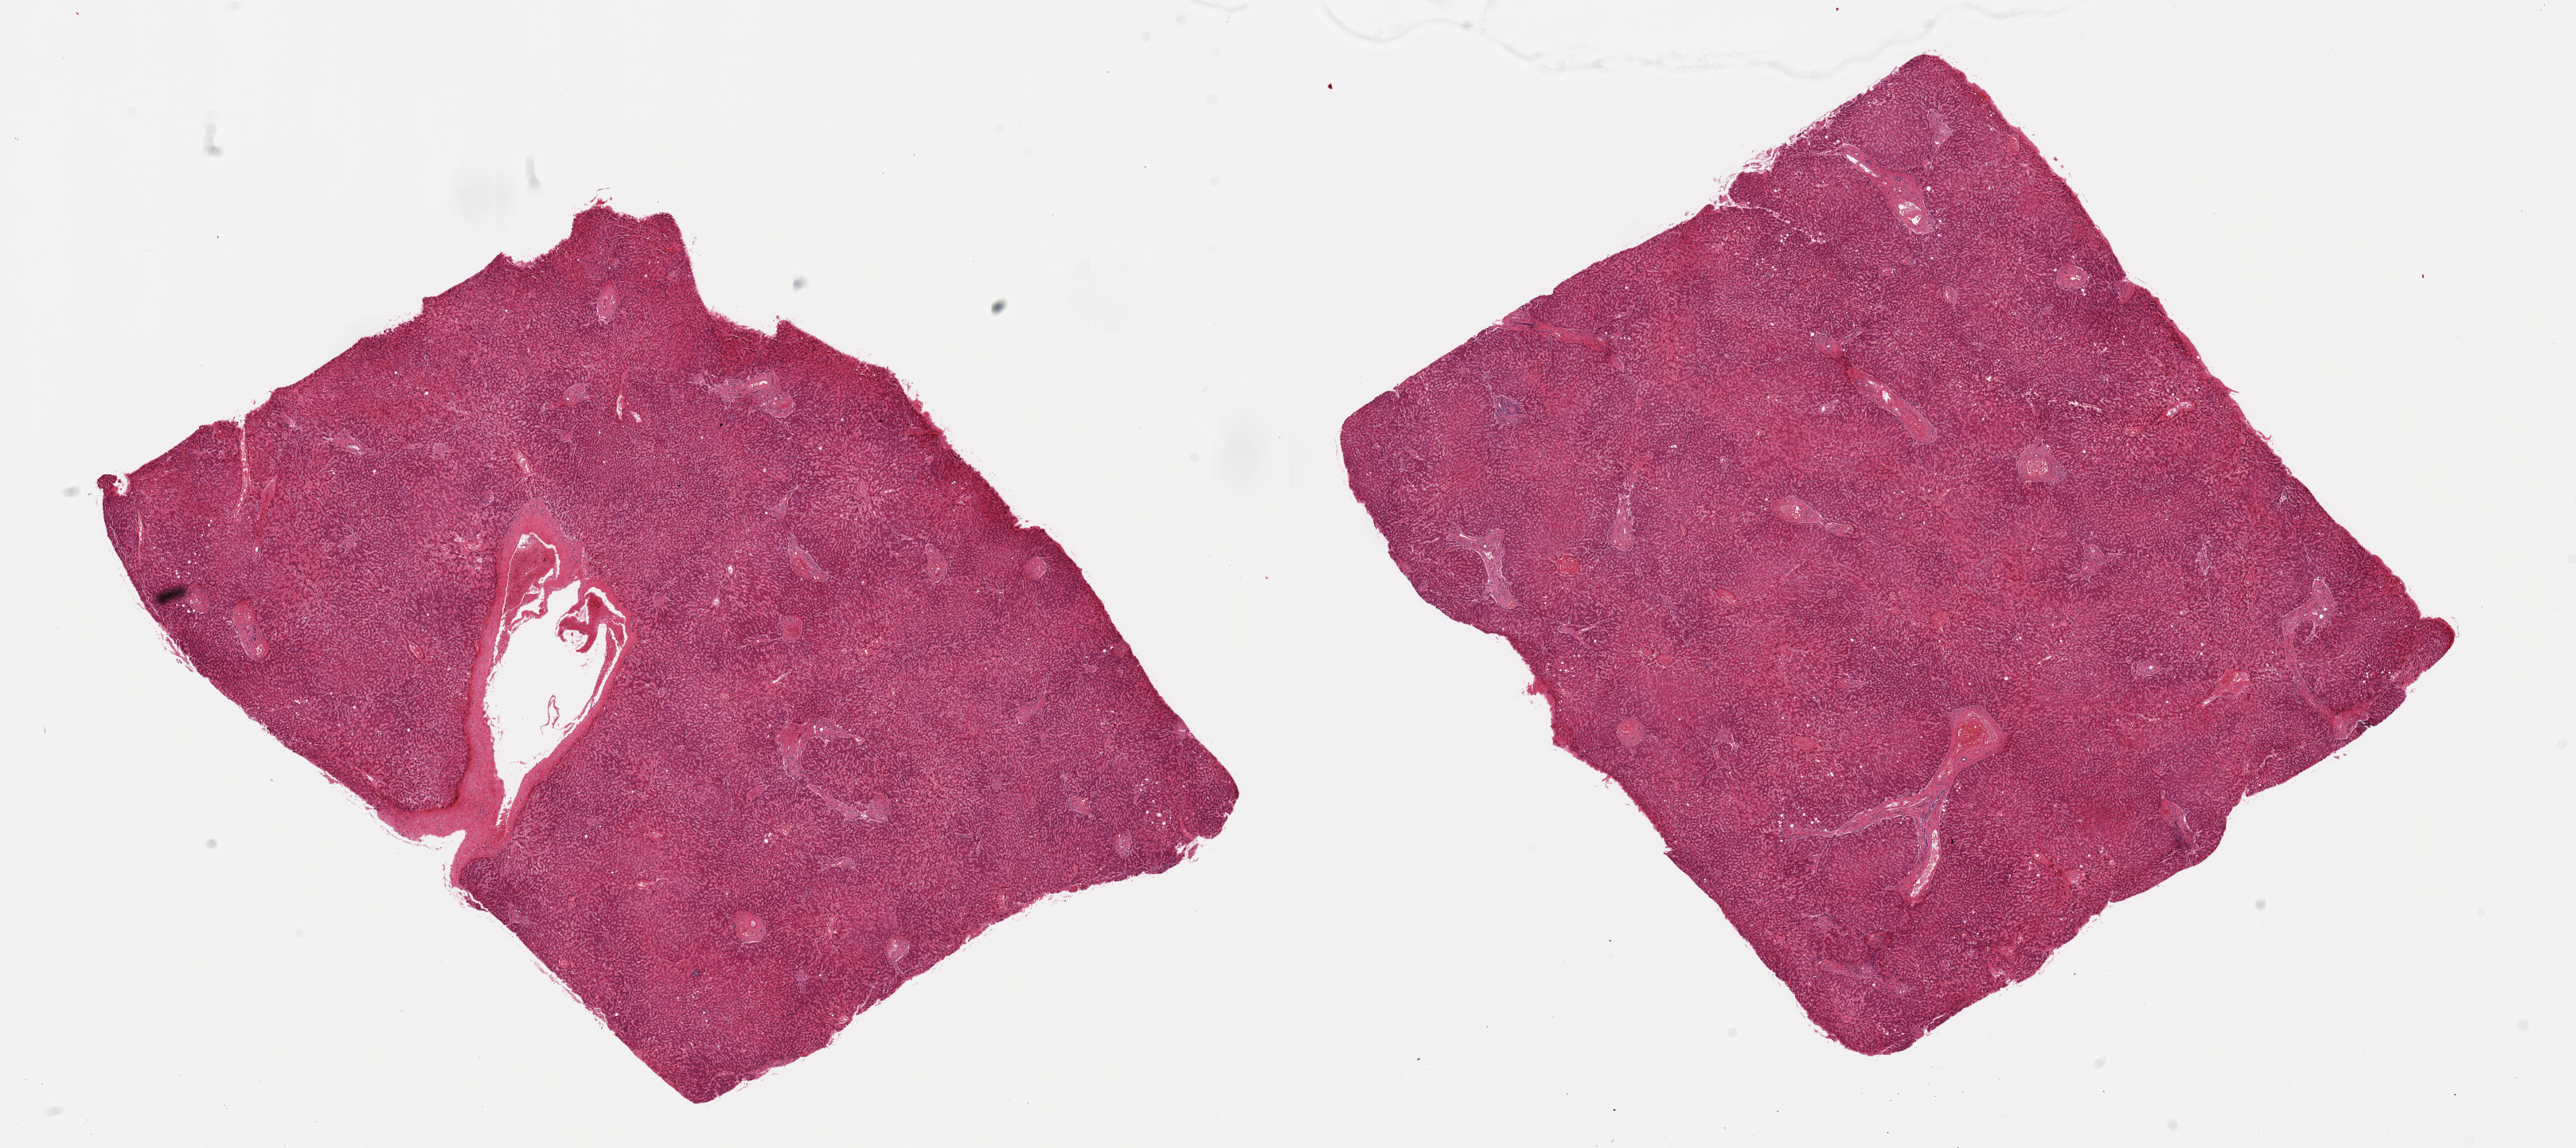
Digitized haematoxylin and eosin-stained section, a low-resolution overview of the entire scanned area, about 25.6 x 11.4 mm, PAXgene-fixed, paraffin-embedded tissue, target tissue: liver, donor tissue sample. Donor: female.
Review note (as recorded): 2 pieces; congestion, focal portal chronic inflammation.